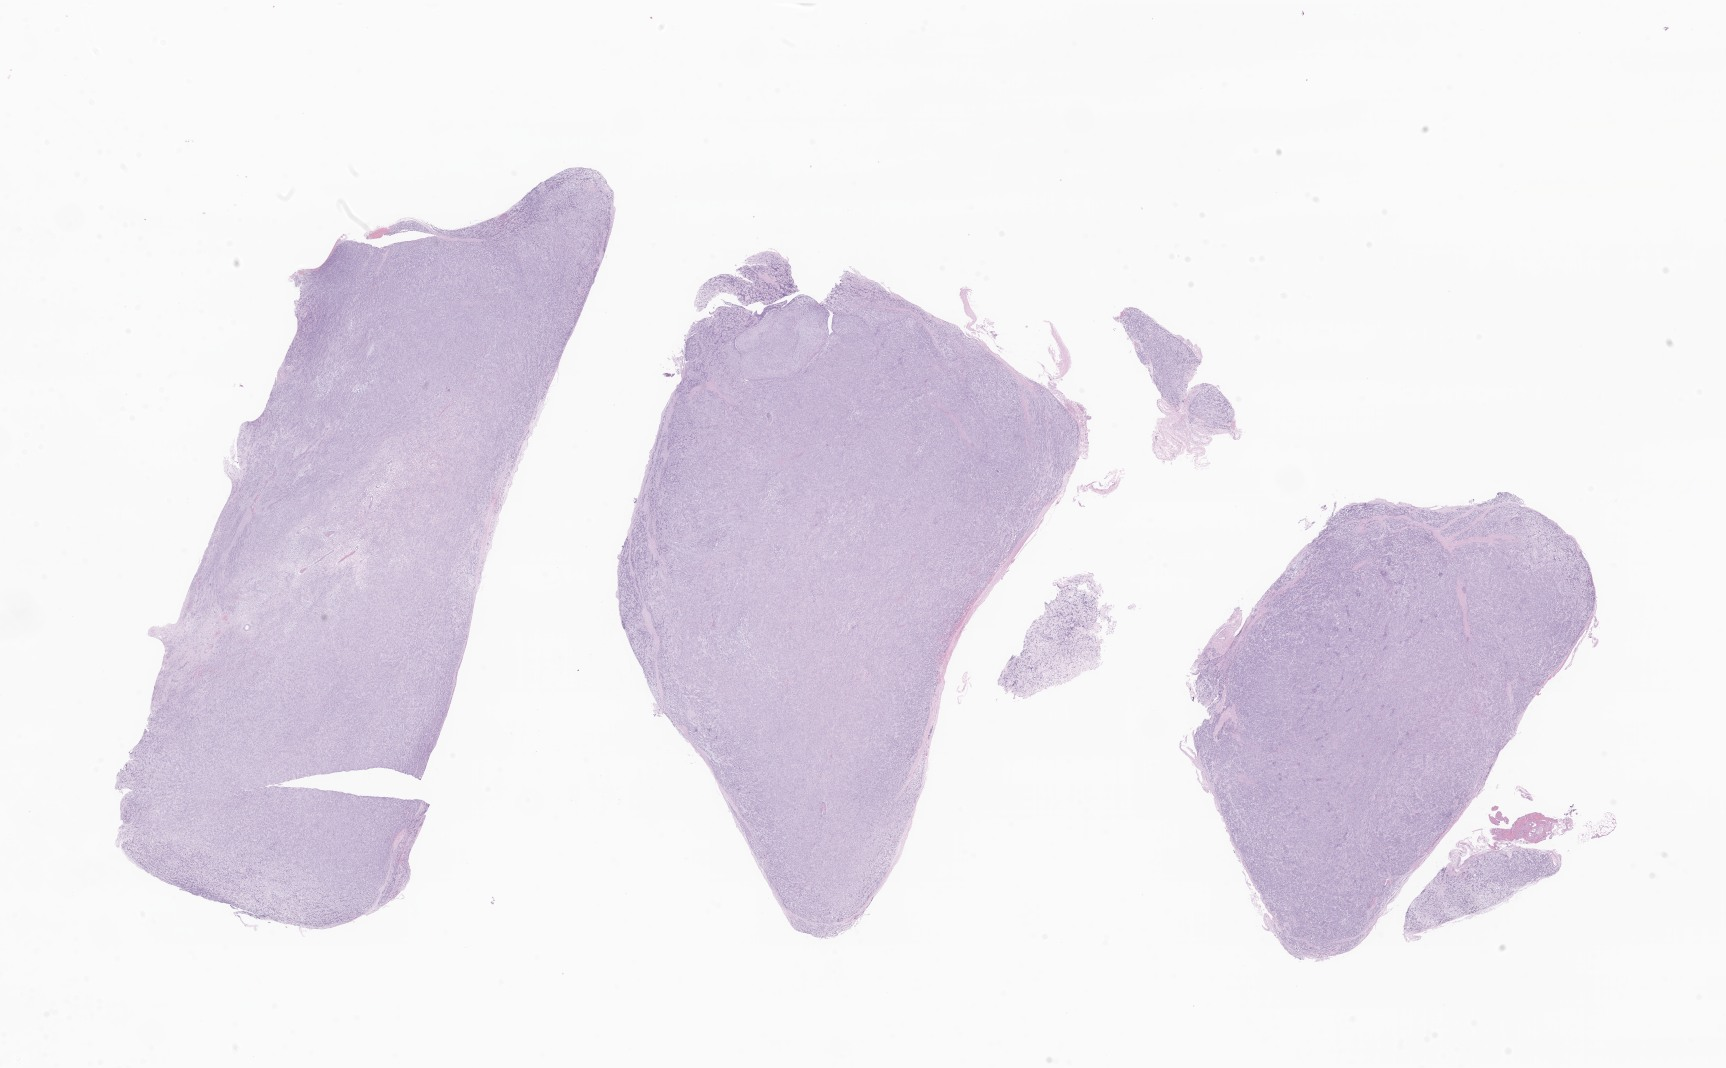
Whole-slide image, hematoxylin and eosin (H&E) stain of tumor tissue from the spinal cord — whole scanned area (about 29.1 x 18.0 mm) shown as a low-resolution overview. Formalin-fixed paraffin-embedded section. Patient female; age 91 months (7 years 7 months).
Recorded diagnosis: Neoplasm, uncertain whether benign or malignant.